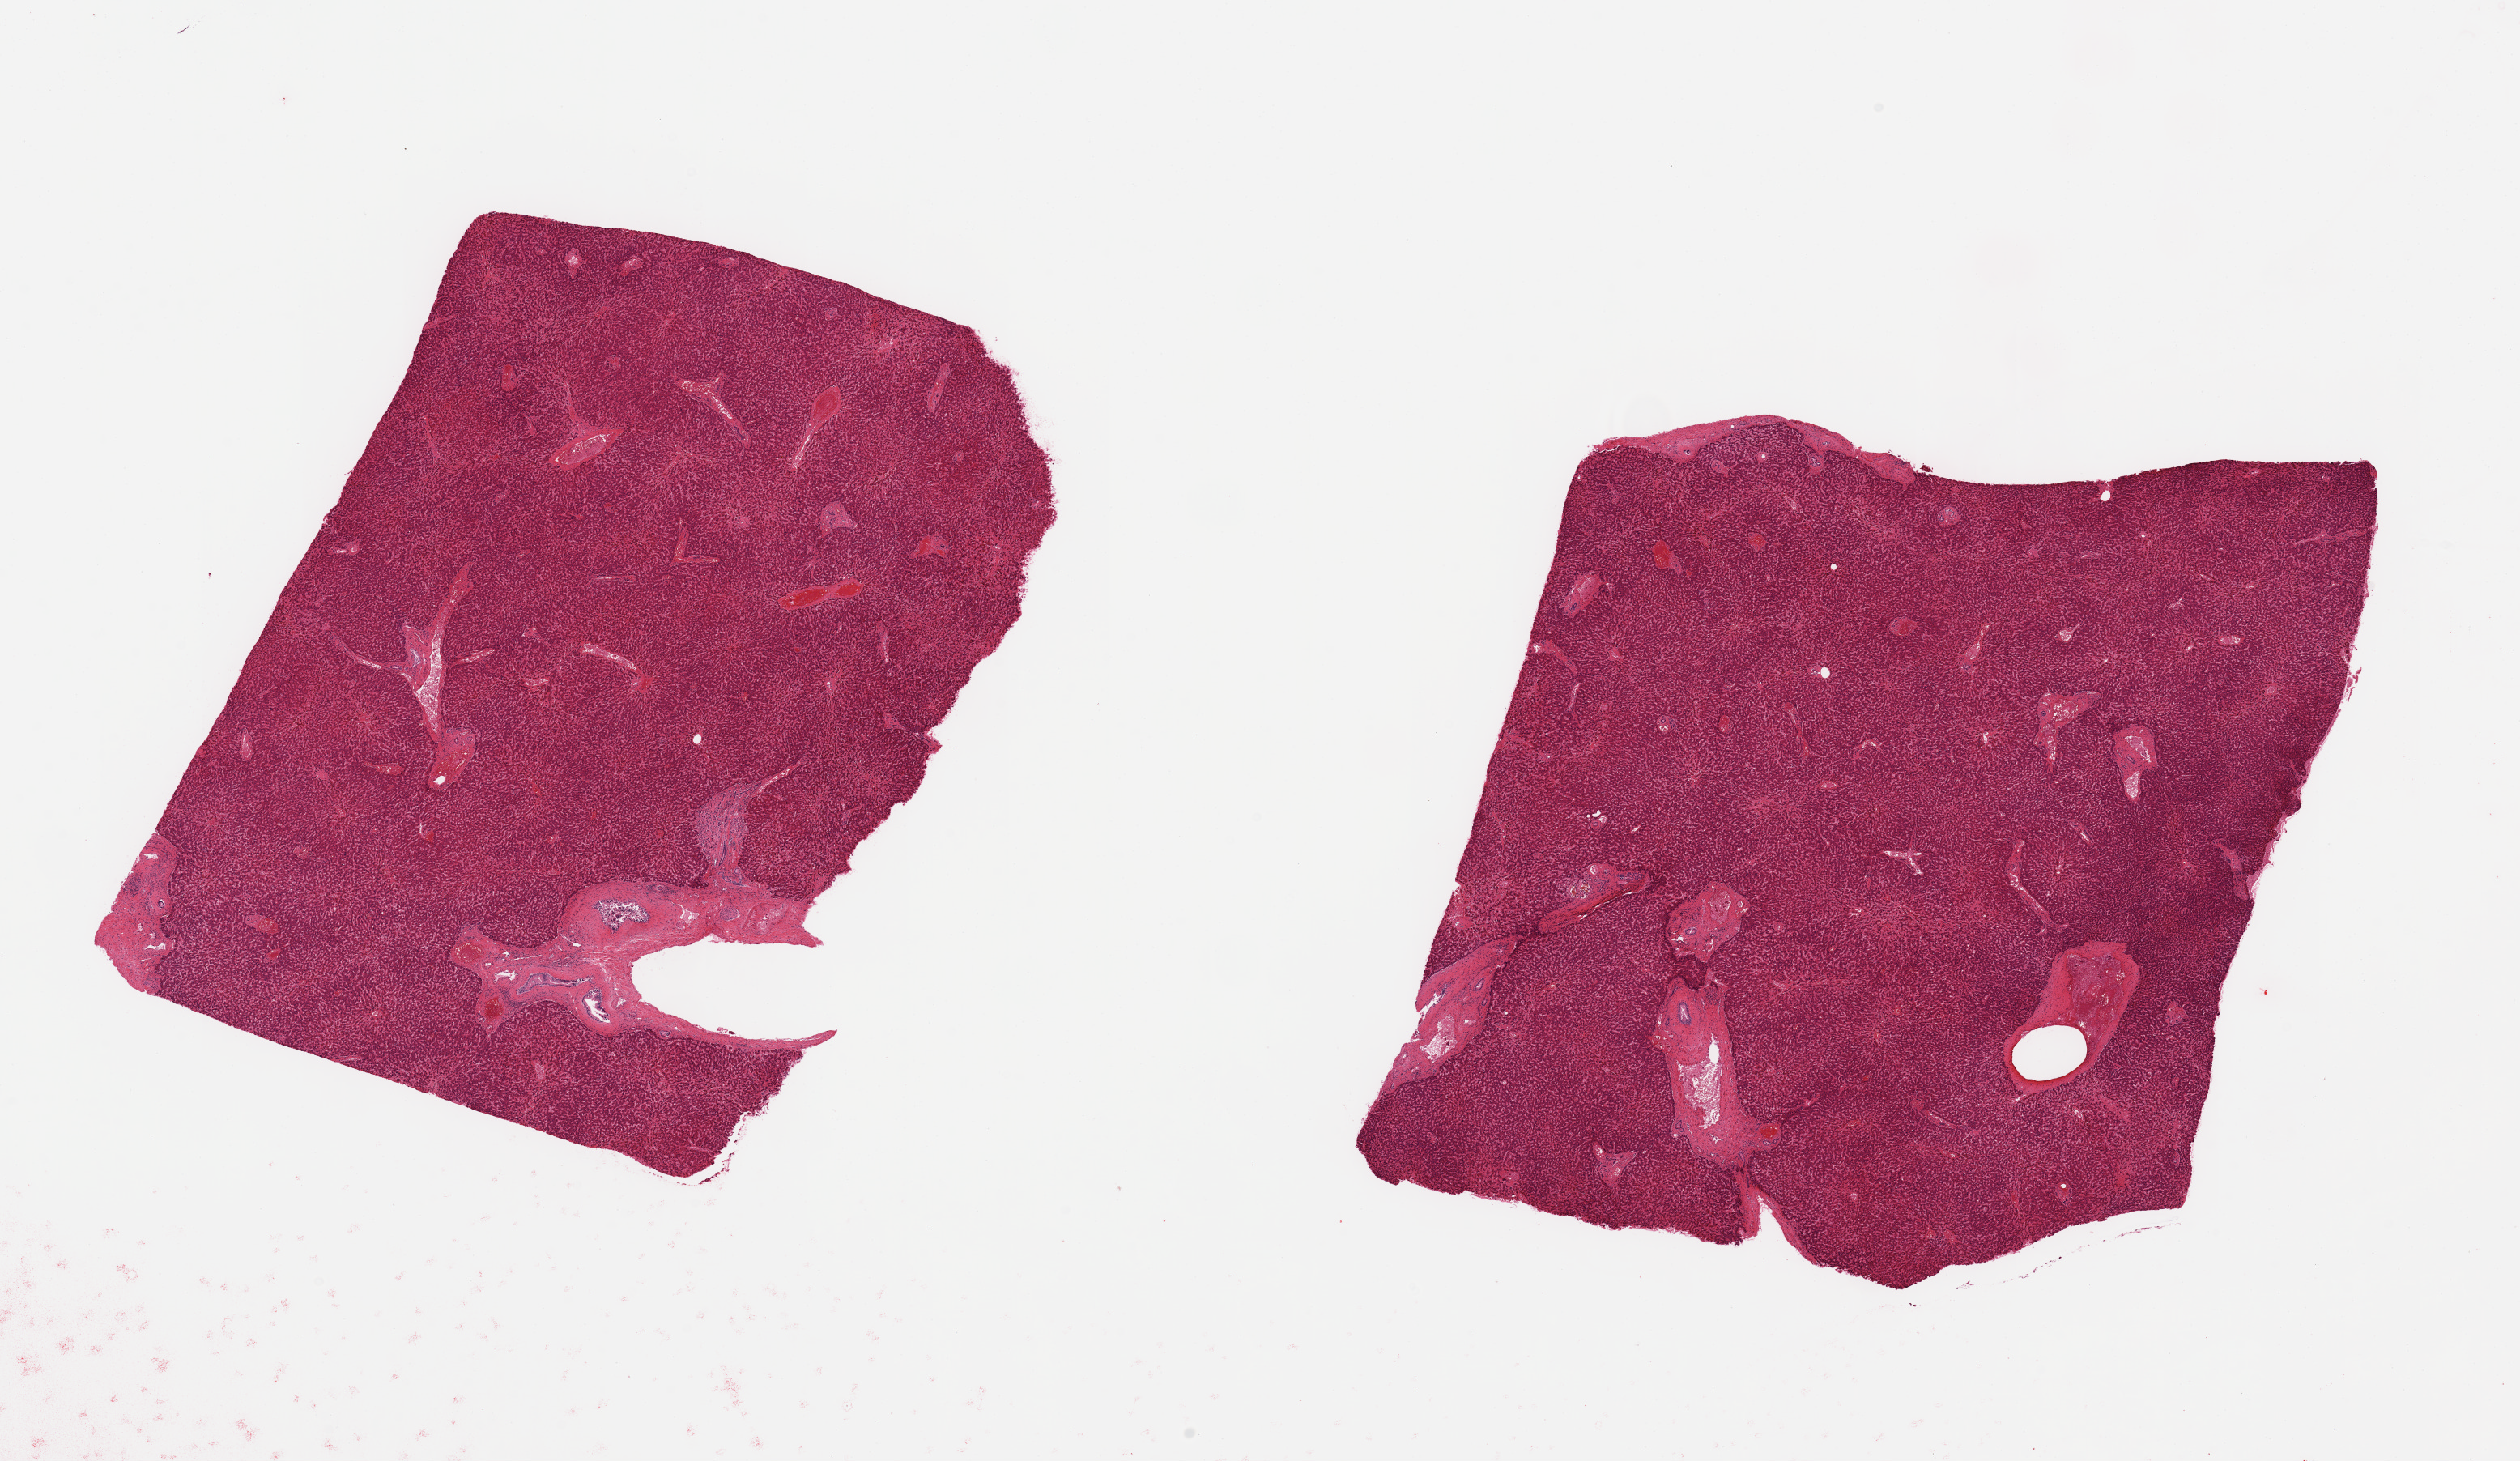
Whole-slide image, haematoxylin and eosin stain, shown as a low-resolution overview of the whole scanned area (about 24.6 x 14.3 mm). PAXgene-fixed, paraffin-embedded tissue. Sampled site (target tissue): liver. Tissue donor sample.
Pathologist's review note for this sample: 2 pieces; several bile duct hamartomas occupy 5%.